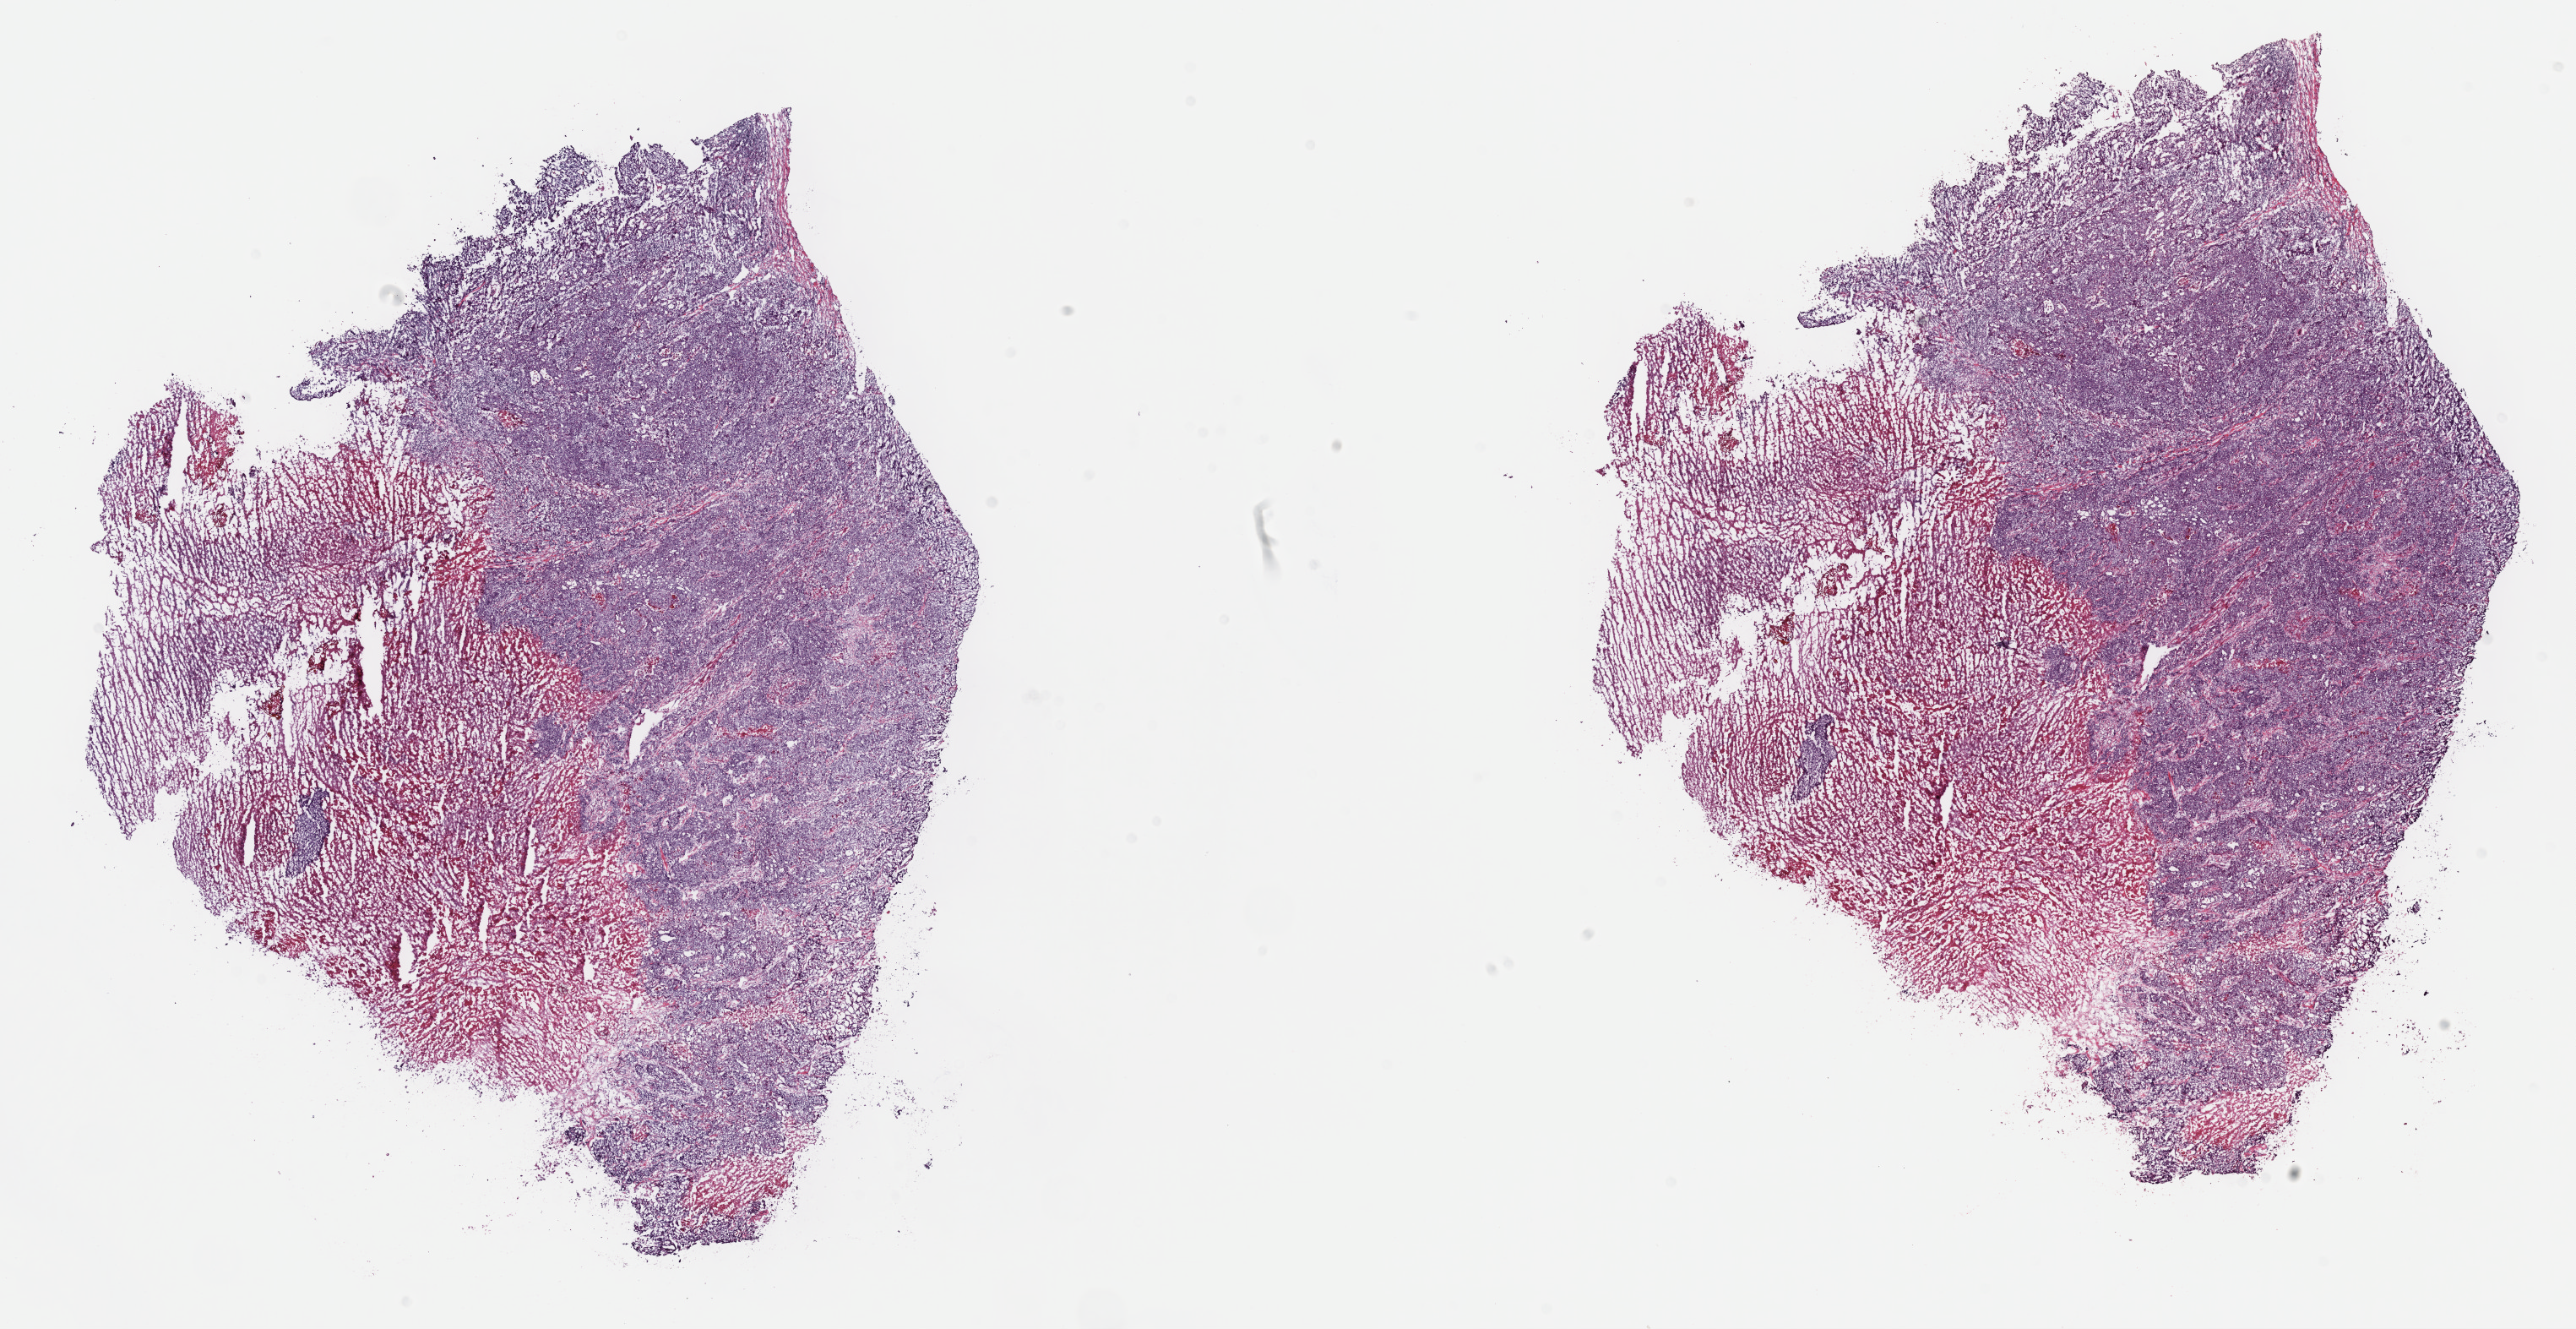
H&E whole-slide image — a low-resolution overview of the entire scanned area, about 24.7 x 12.7 mm. Frozen section from the top of the tissue portion. Bladder, primary tumour sample. Male, age 73 years at initial diagnosis. Histologic grade: high grade. Composition of this section per pathologist review: tumour cells 65%, tumour nuclei 65%, normal cells 0%, stromal cells 15%, necrosis 20%. Inflammatory infiltration, as recorded: lymphocyte infiltration 2%, monocyte infiltration 1%, neutrophil infiltration 4%.
AJCC pathologic stage: II (6th edition). Lymph nodes positive (case pathology): 0 of 73 examined. Diagnosis: Transitional cell carcinoma.